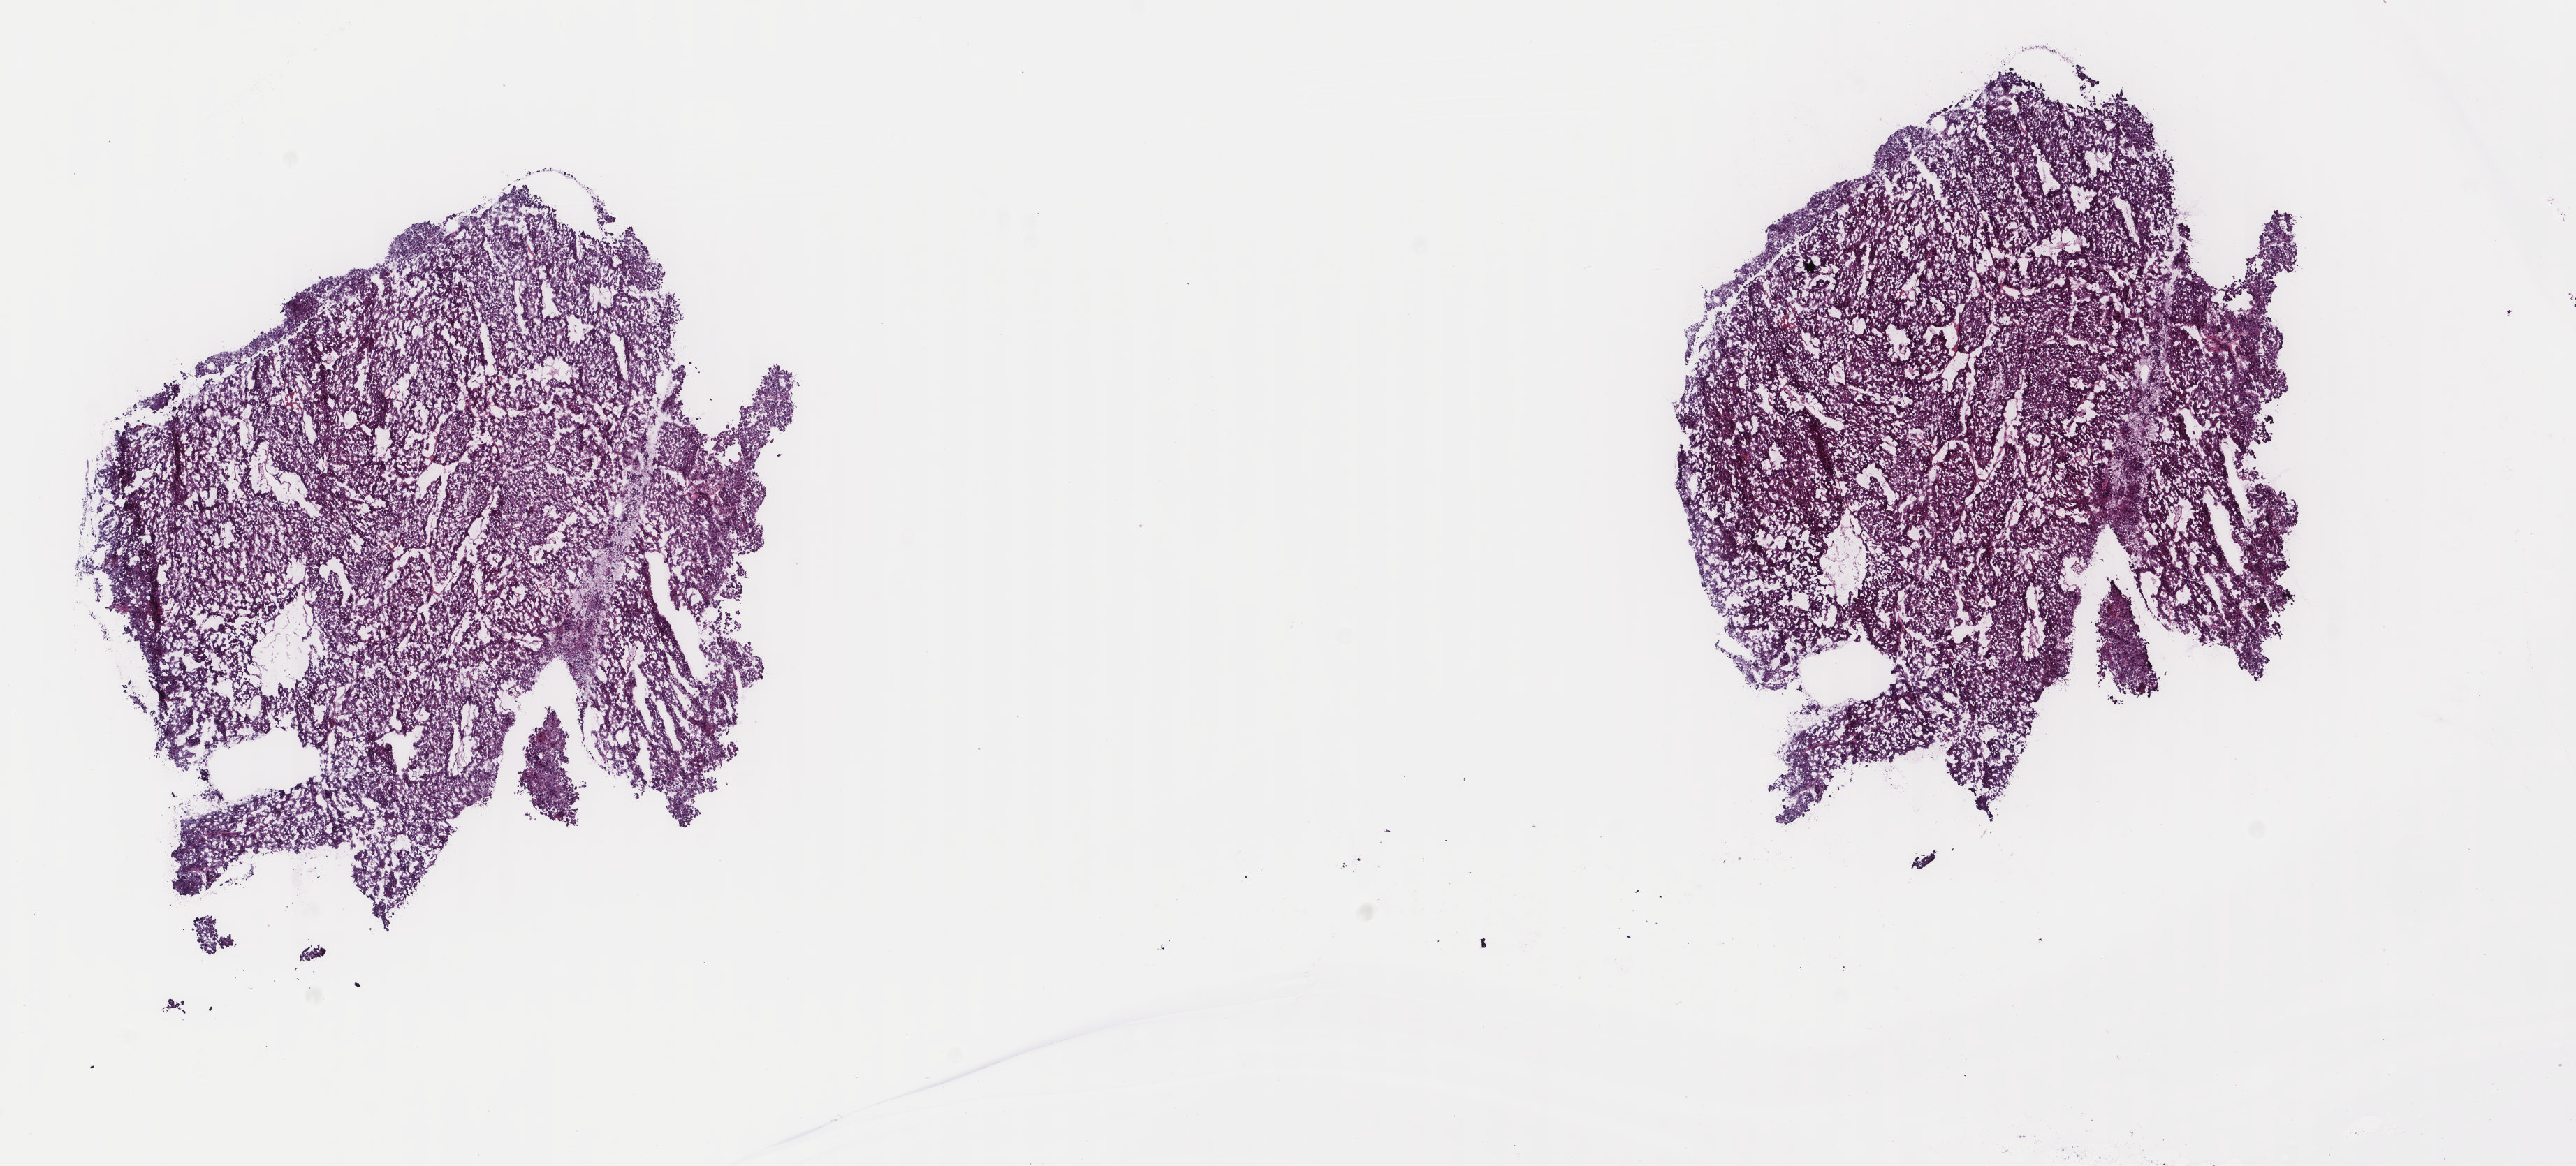
Digitized H&E tissue section (whole slide) — low-resolution overview of the scanned area, about 14.6 x 6.6 mm; frozen section; liver, primary tumour sample. Patient: male, age at initial diagnosis 64 years. Histologic grade: G2 (moderately differentiated). Pathologist review of this section (percent, as recorded): tumour cells 100%, tumour nuclei 90%, normal cells 0%, stromal cells 0%, necrosis 0%. Inflammatory infiltration, as recorded: lymphocyte infiltration 0%, monocyte infiltration 0%, neutrophil infiltration 0%.
• pathologic diagnosis: Hepatocellular carcinoma, NOS
• AJCC pathologic stage: I (6th edition)